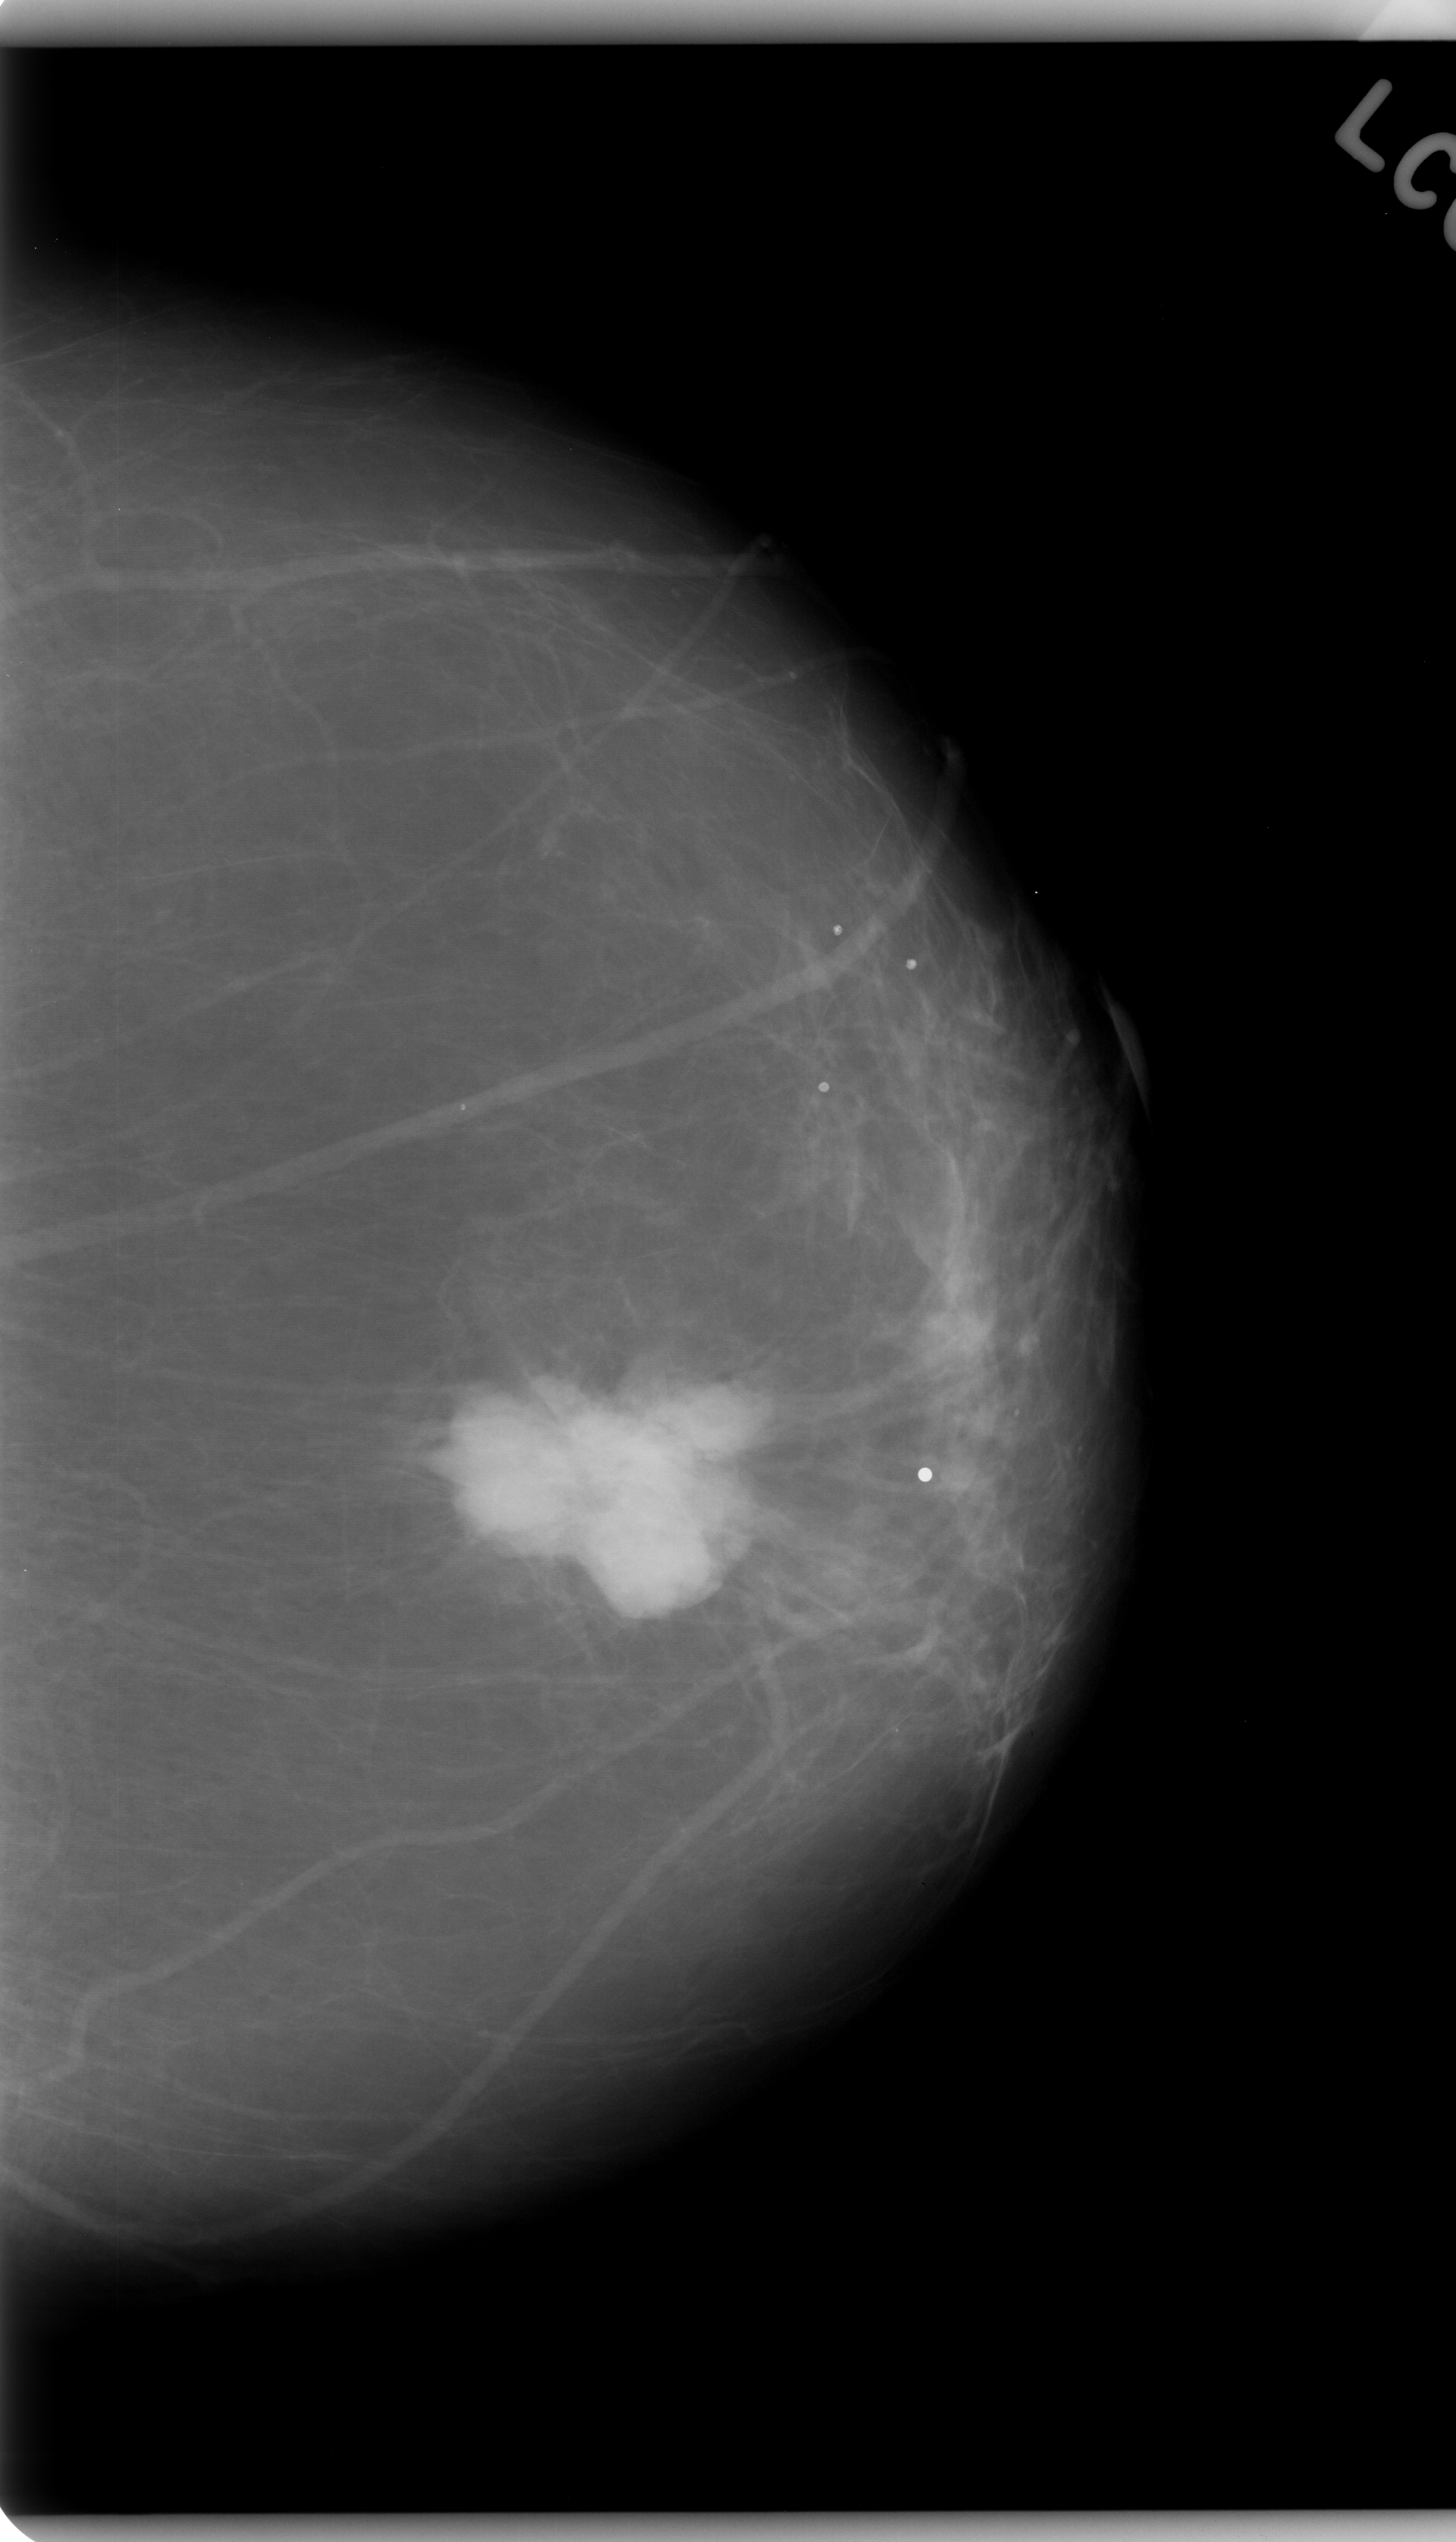
Digitized screen-film mammogram. Left breast. Craniocaudal (CC) view. Breast composition: almost entirely fatty (BI-RADS density category 1 of 4). 1456 × 2542 image matrix.
Expert-marked regions of interest on this image (one box per marked abnormality):
- mass, shape lobulated, margins microlobulated; BI-RADS assessment category 5; subtlety rating 5 on a 1 (subtle) to 5 (obvious) scale; pathology (as recorded): malignant: bounding box <443,1365,751,1618> (left, top, right, bottom; pixels)